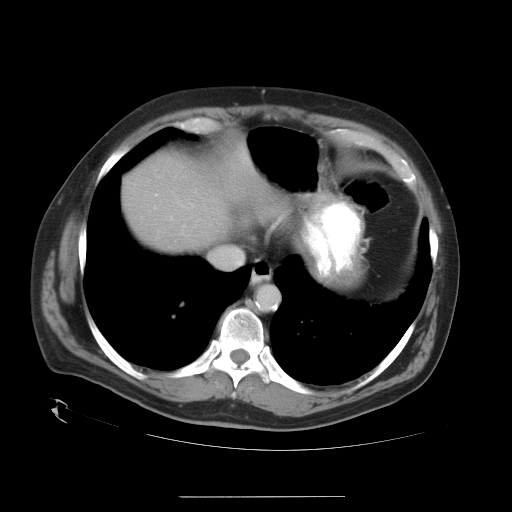
Contrast-enhanced abdominal CT, one axial slice. Slice 30 of 35 in the series (ordered by position). Reconstruction kernel STANDARD. Intravenous contrast given. Soft-tissue window (W 400 / L 40 HU). 7.5 mm slice thickness. 512 × 512 image matrix. Male patient, age 67 years. Case-level facts recorded for this patient, not image findings: diagnosis: colorectal cancer liver metastases, imaged before liver resection; multiple liver metastases: no; largest metastasis: 2.3 cm; disease in both lobes: no.
Outlined on this slice (expert manual segmentation):
- hepatic veins: bounding box [x1, y1, x2, y2] px = [221, 249, 242, 258]
- liver: [122, 157, 229, 252]
- planned liver remnant (the part of the liver to remain after resection): [122, 157, 229, 252]